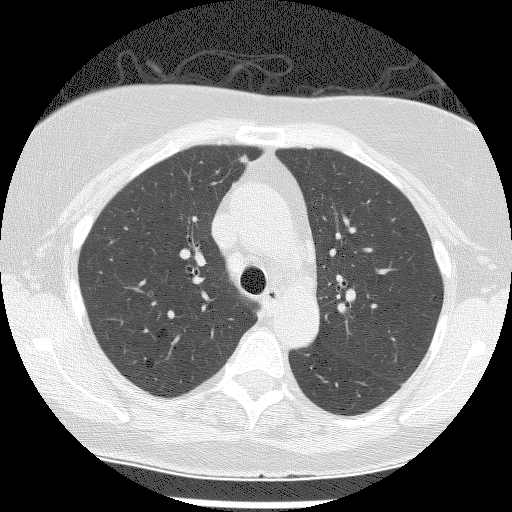
Axial slice from a low-dose chest CT screening exam, second screening round (one year after baseline), lung window (W 1500 / L -600 HU), 2.5 mm slice thickness, lung (sharp) reconstruction kernel (BONE), slice 47 of 149 in the series, 512 × 512 image matrix, field of view 300 × 300 mm. Female participant, aged 61 years at enrolment.
Expert reader's lesion annotation, box from (x=229, y=149) to (x=259, y=172) px. Screening reader's record for this exam (one nodule recorded; not confirmed to be the boxed lesion): non-calcified nodule or mass ≥4 mm, right upper lobe, 5 × 4 mm, smooth margins, soft tissue attenuation, pre-existing on the prior screen: no. Official screen result: positive, other. Lung cancer was diagnosed 244 days after this screen: adenocarcinoma, NOS, right upper lobe, moderately differentiated (G2), stage IA (AJCC 6th edition), 8 mm at pathology.